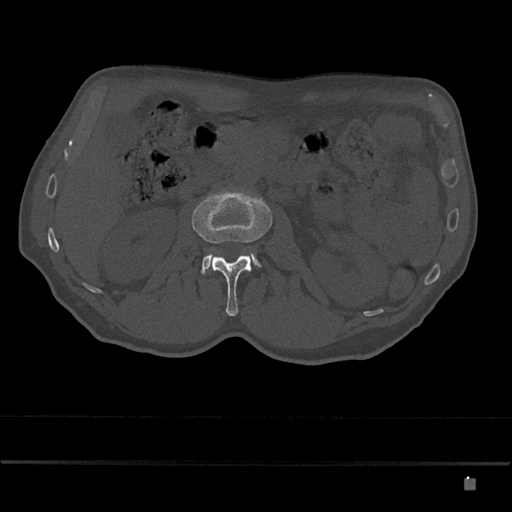
CT including the spine, one axial slice; position 459 of 797 along the scan axis; reconstruction kernel Br40s/3; bone window (W 1800 / L 400 HU); 0.5 mm slice thickness; 512 × 512 image matrix, field of view 390 × 390 mm. Male patient, age 72 years. From the clinical record (not read from this slice): primary cancer: prostate.
Outlined on this slice (semi-automatically segmented with operator editing):
- L2 vertebra: box from (x=192, y=189) to (x=272, y=316) px
- L3 vertebra: (x=201, y=253)–(x=261, y=274)